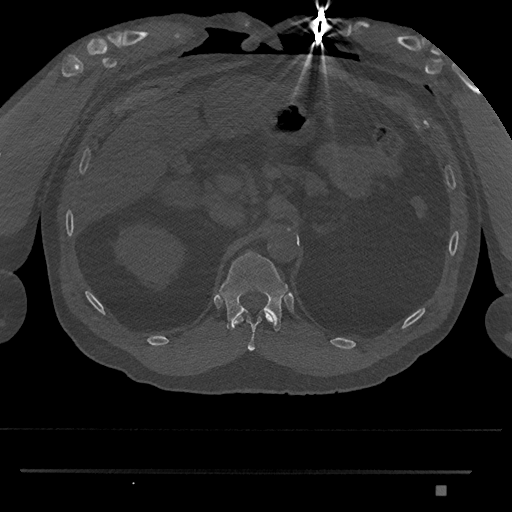
CT including the spine, one axial slice. Reconstruction kernel Br40s/3. Bone window (W 1800 / L 400 HU). 512 × 512 image matrix, field of view 429 × 429 mm. Male patient, age 65 years. From the clinical record (not read from this slice): primary cancer: prostate.
Structures marked on this image (semi-automatic segmentation, software-assisted and operator-edited):
- T11 vertebra: bounding box <235,310,273,351> (left, top, right, bottom; pixels)
- T12 vertebra: <219,251,288,331>